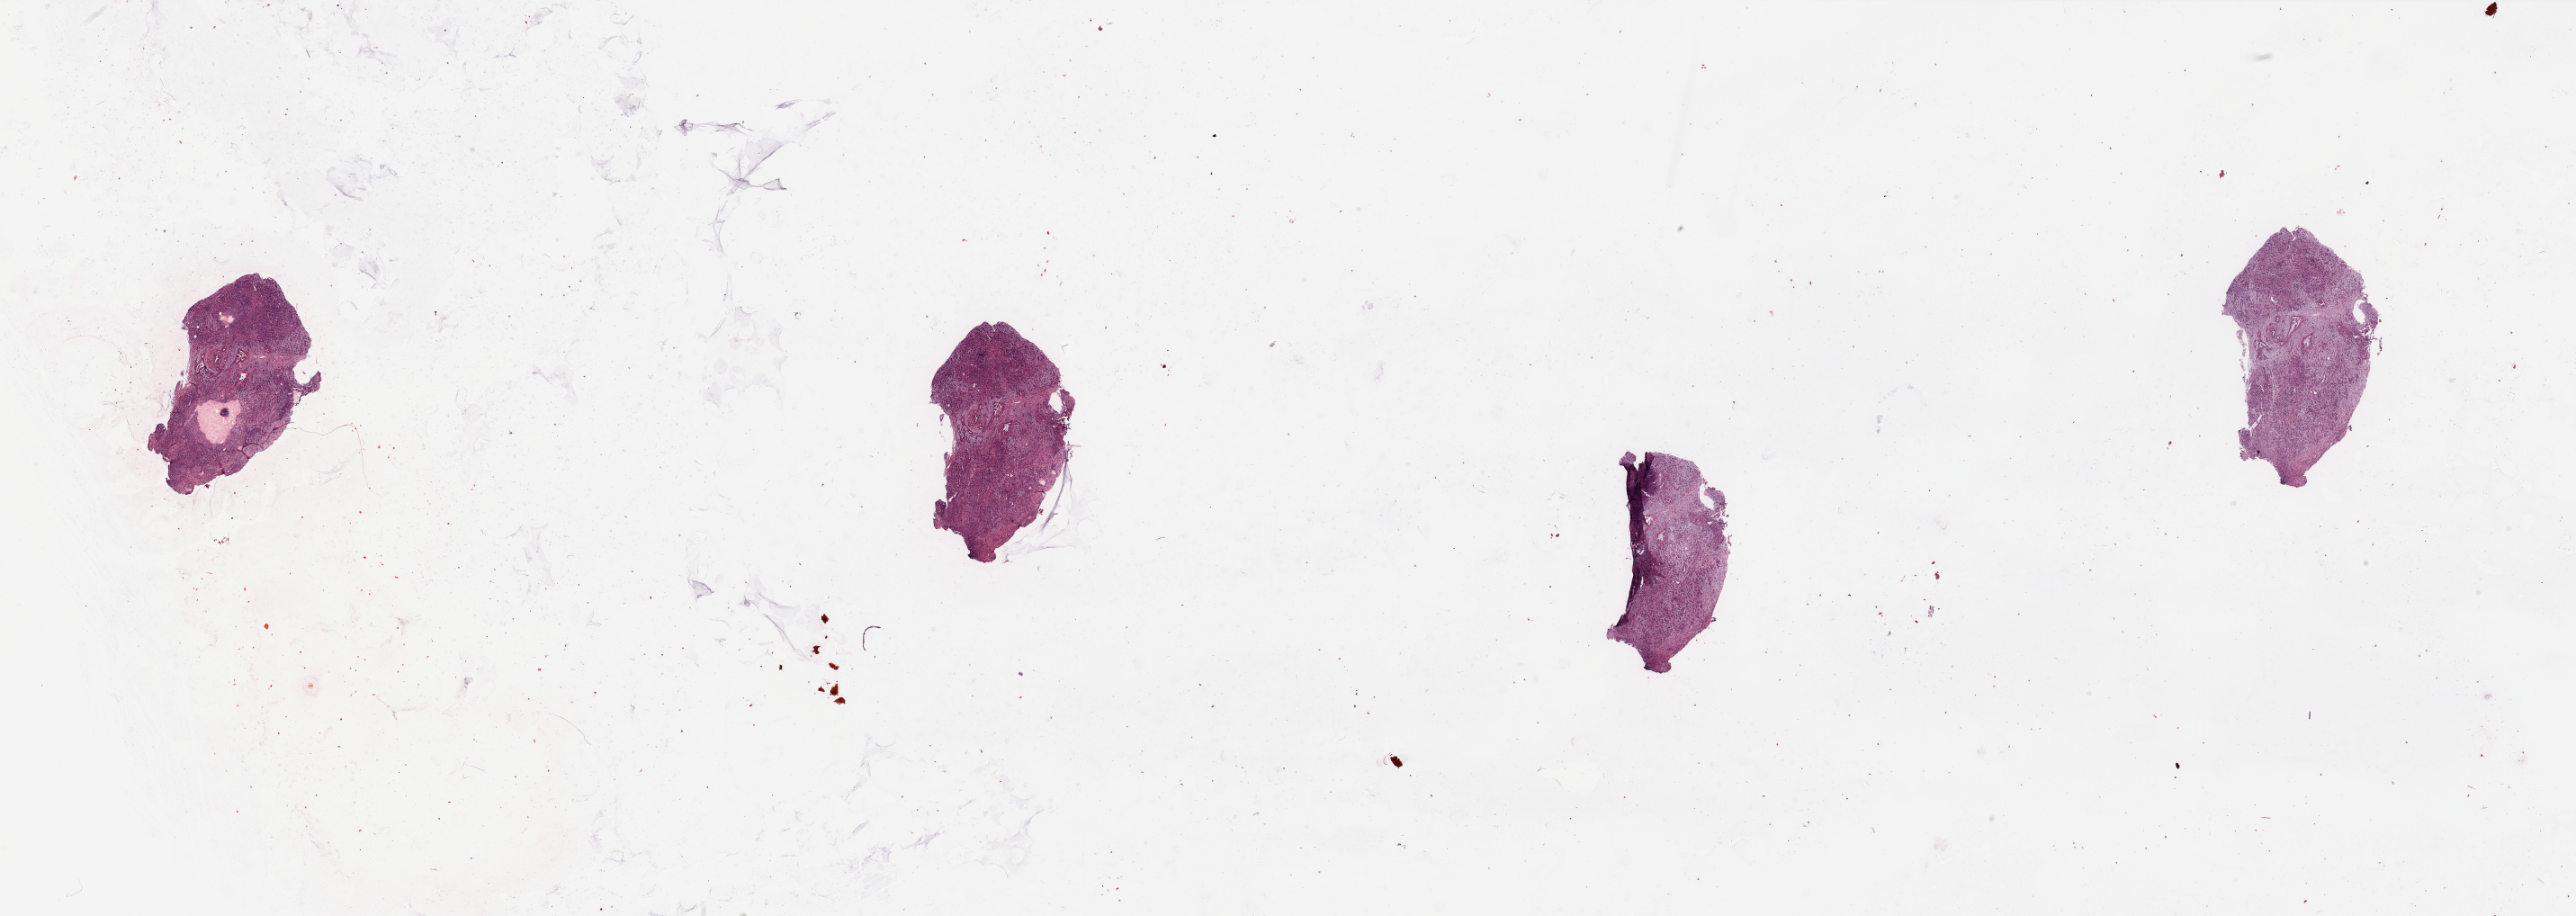
Whole-slide histology image, H&E-stained — low-resolution overview of the scanned area, about 45.3 x 16.1 mm (acquisition: 20x scan). Tumour tissue sample, pancreas. Female, 65 y/o.
Patient diagnosis (cohort enrolment): ductal adenocarcinoma (pancreas). Primary tumour site (as recorded): head.